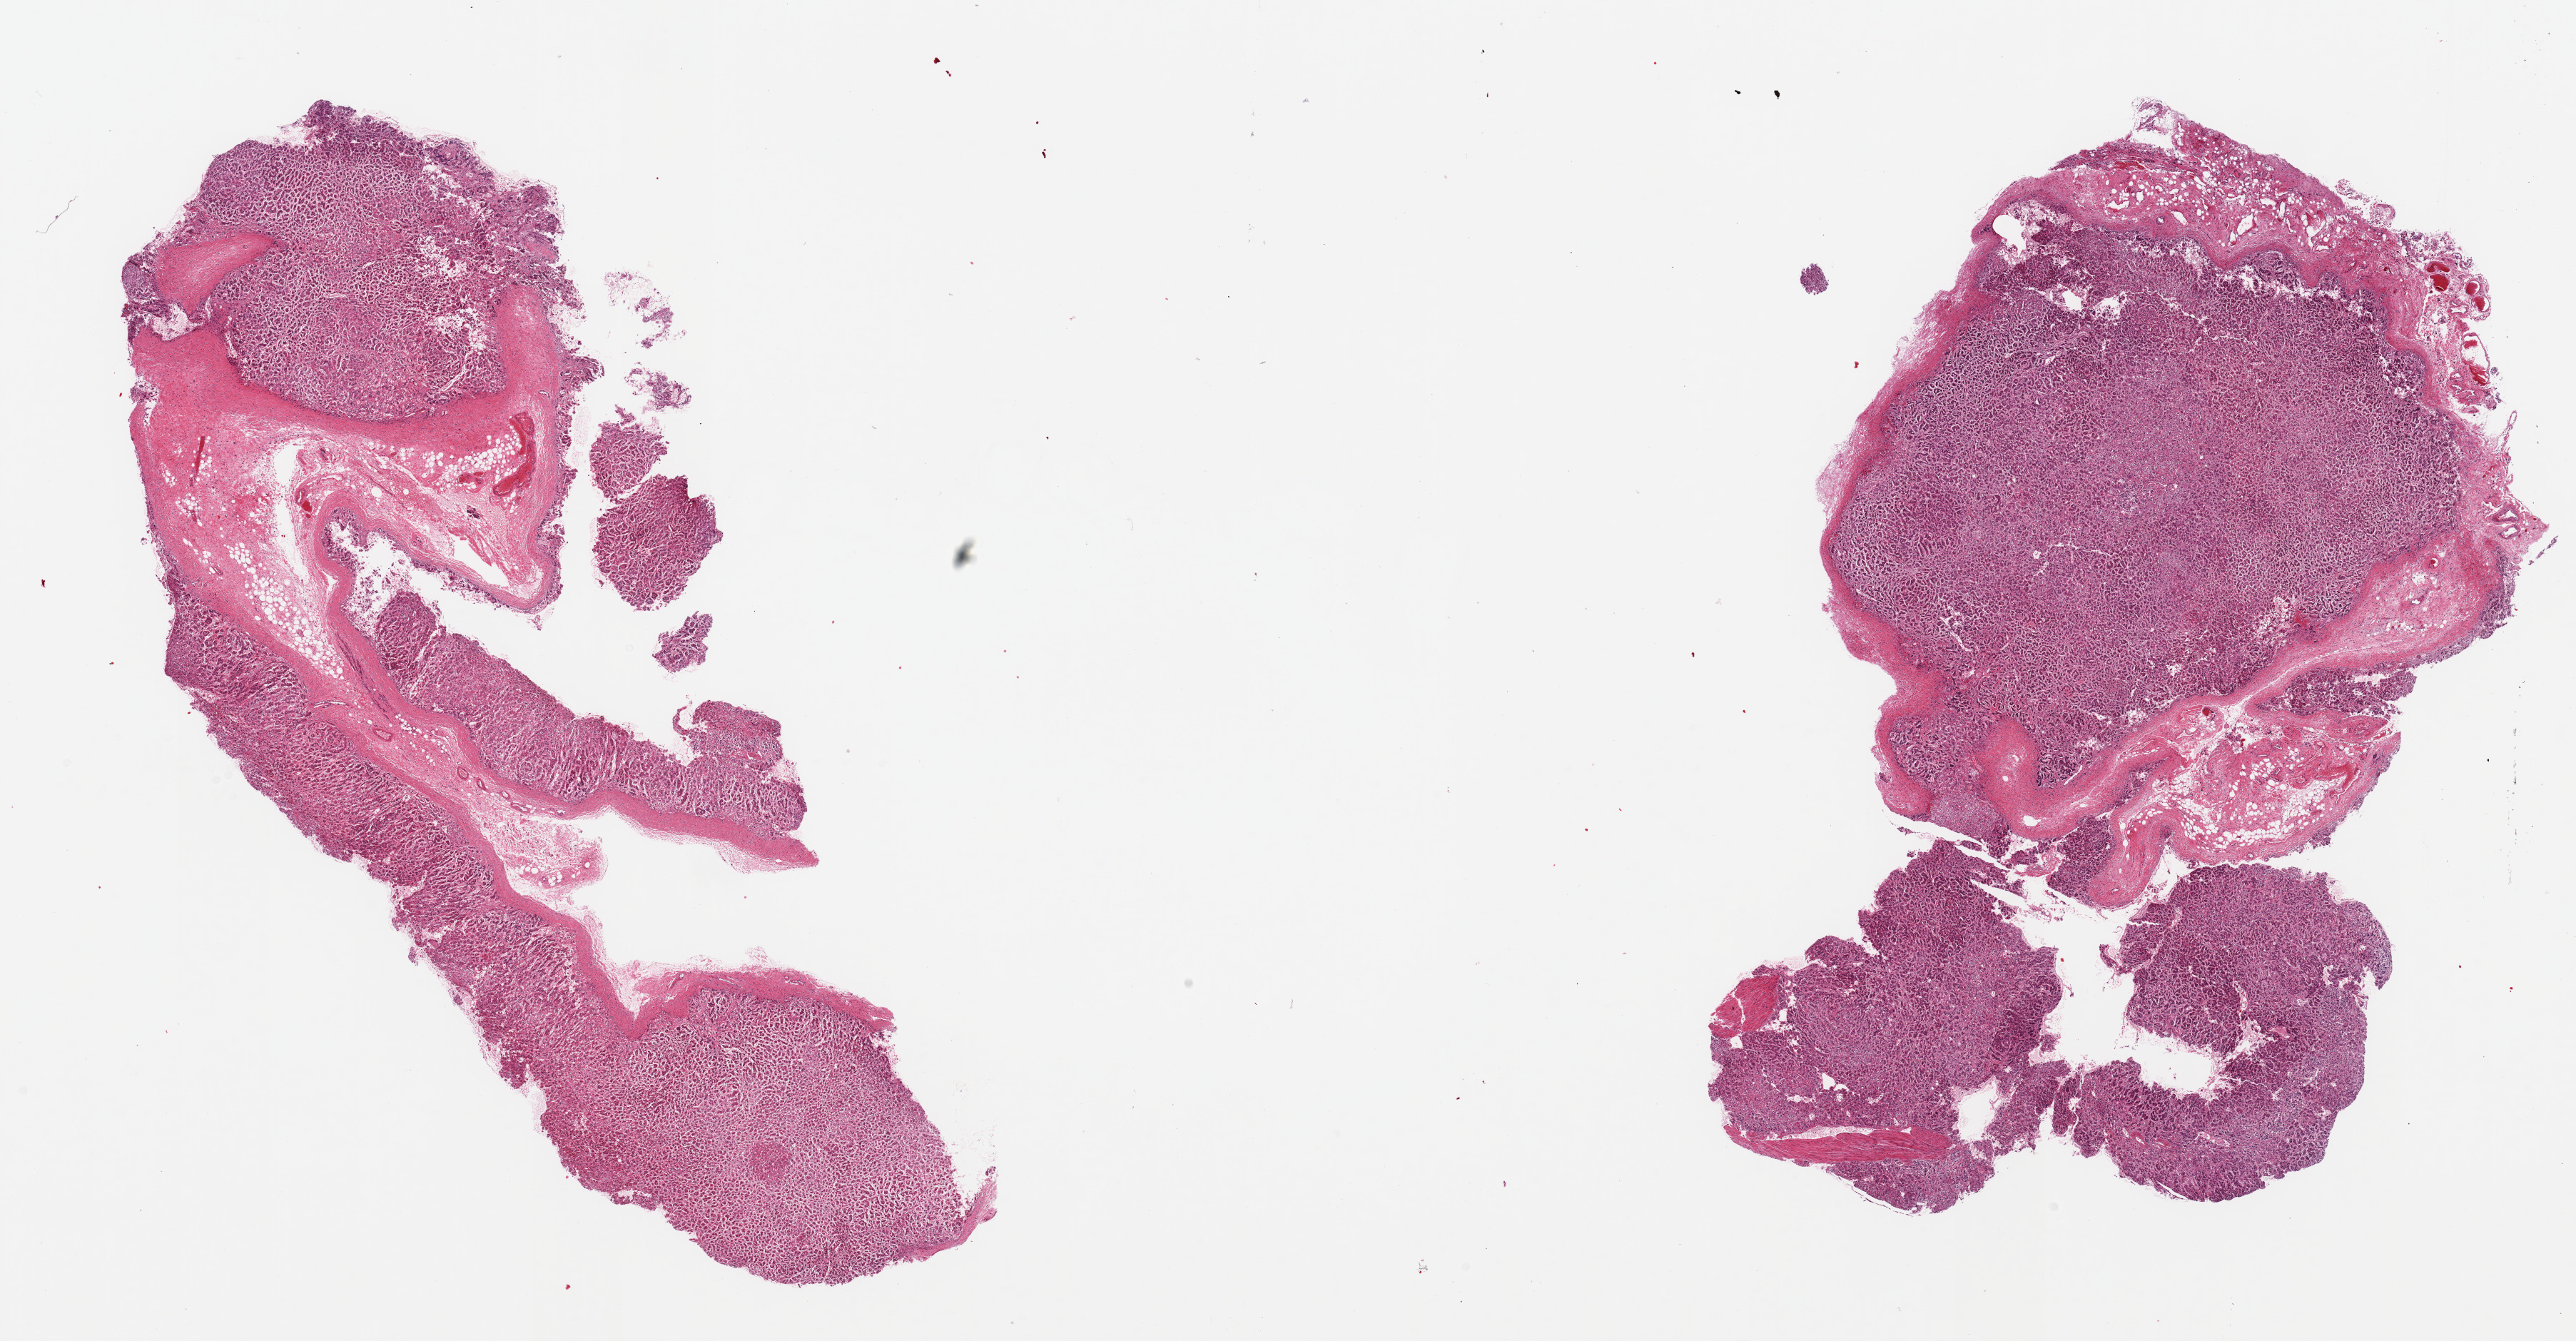
H&E whole-slide image, a low-resolution overview of the entire scanned area, about 28.5 x 14.9 mm; PAXgene-fixed paraffin-embedded (PFPE) section; sampled site (target tissue): adrenal gland; donor tissue sample. Male donor.
Pathologist's review note for this sample: 2 pieces, cortex, ~25% adherent/interstitial fibrous tissue.